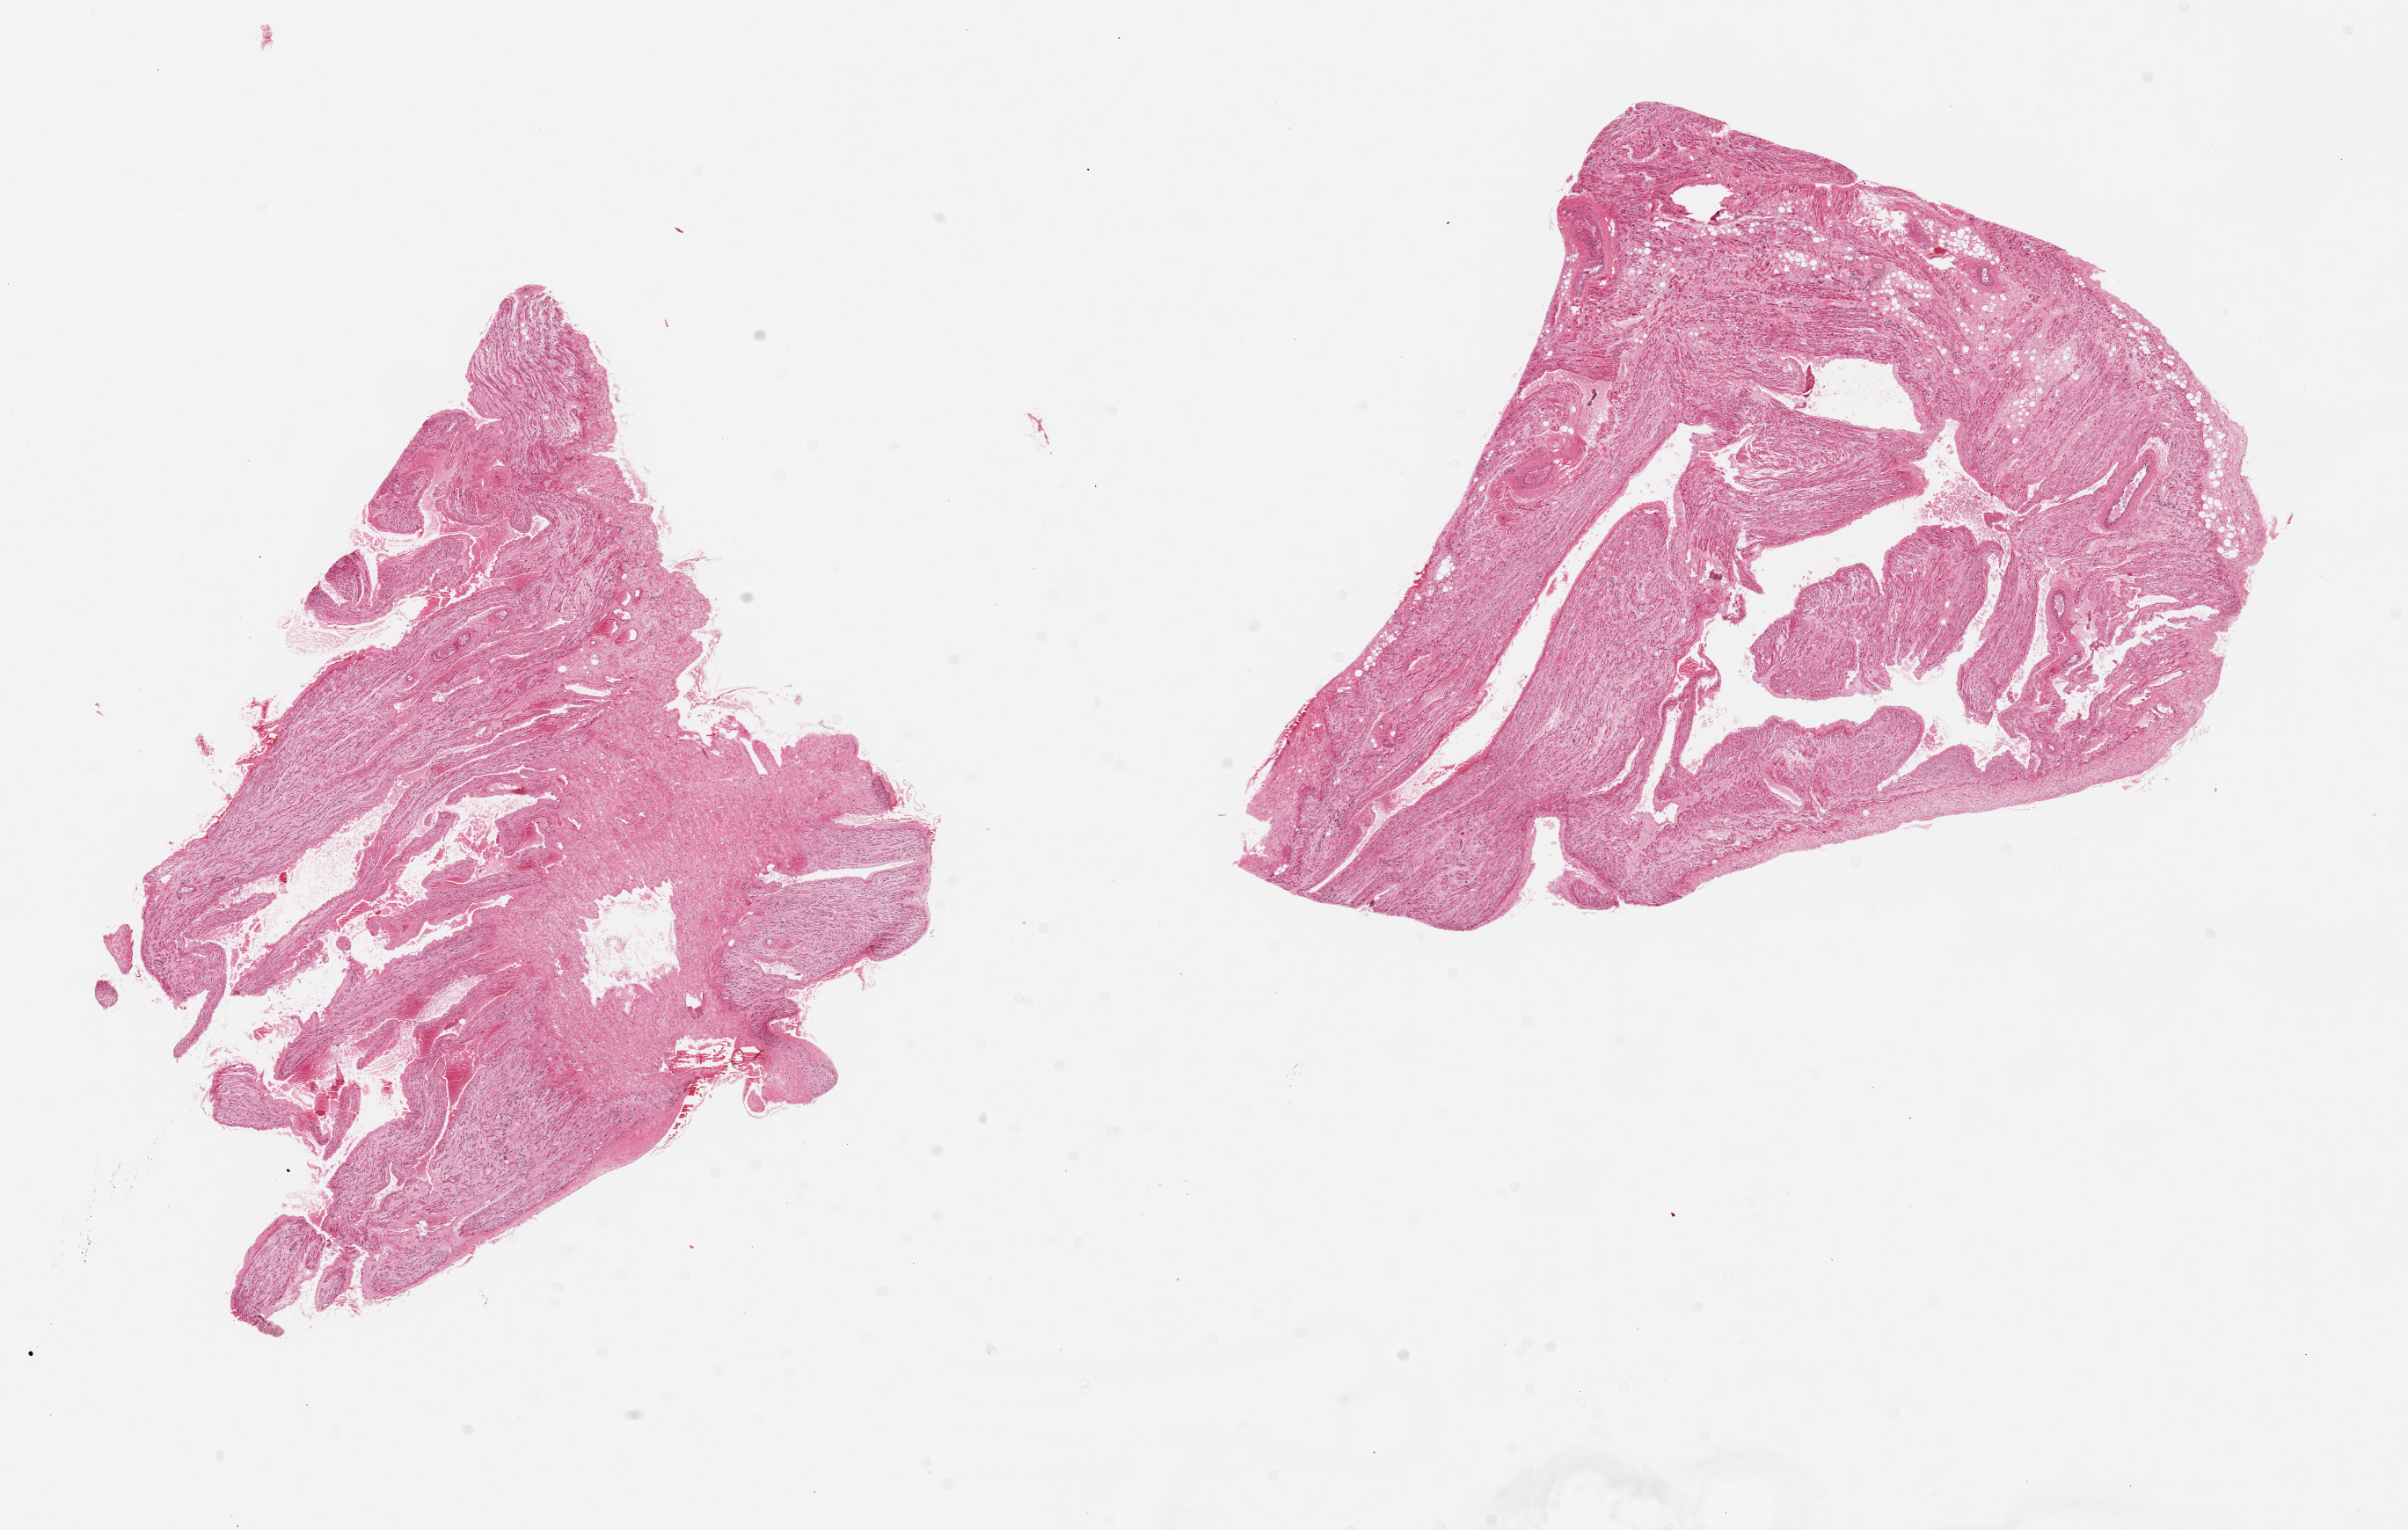
Whole-slide image, hematoxylin and eosin (H&E) stain, a low-resolution overview of the entire scanned area, about 21.7 x 13.8 mm (slide scanned at 20x), PAXgene-fixed, paraffin-embedded tissue, target tissue: auricular appendage, donor tissue sample. Female donor.
Review note (as recorded): 2 pieces, 8x8 & 10x7mm.